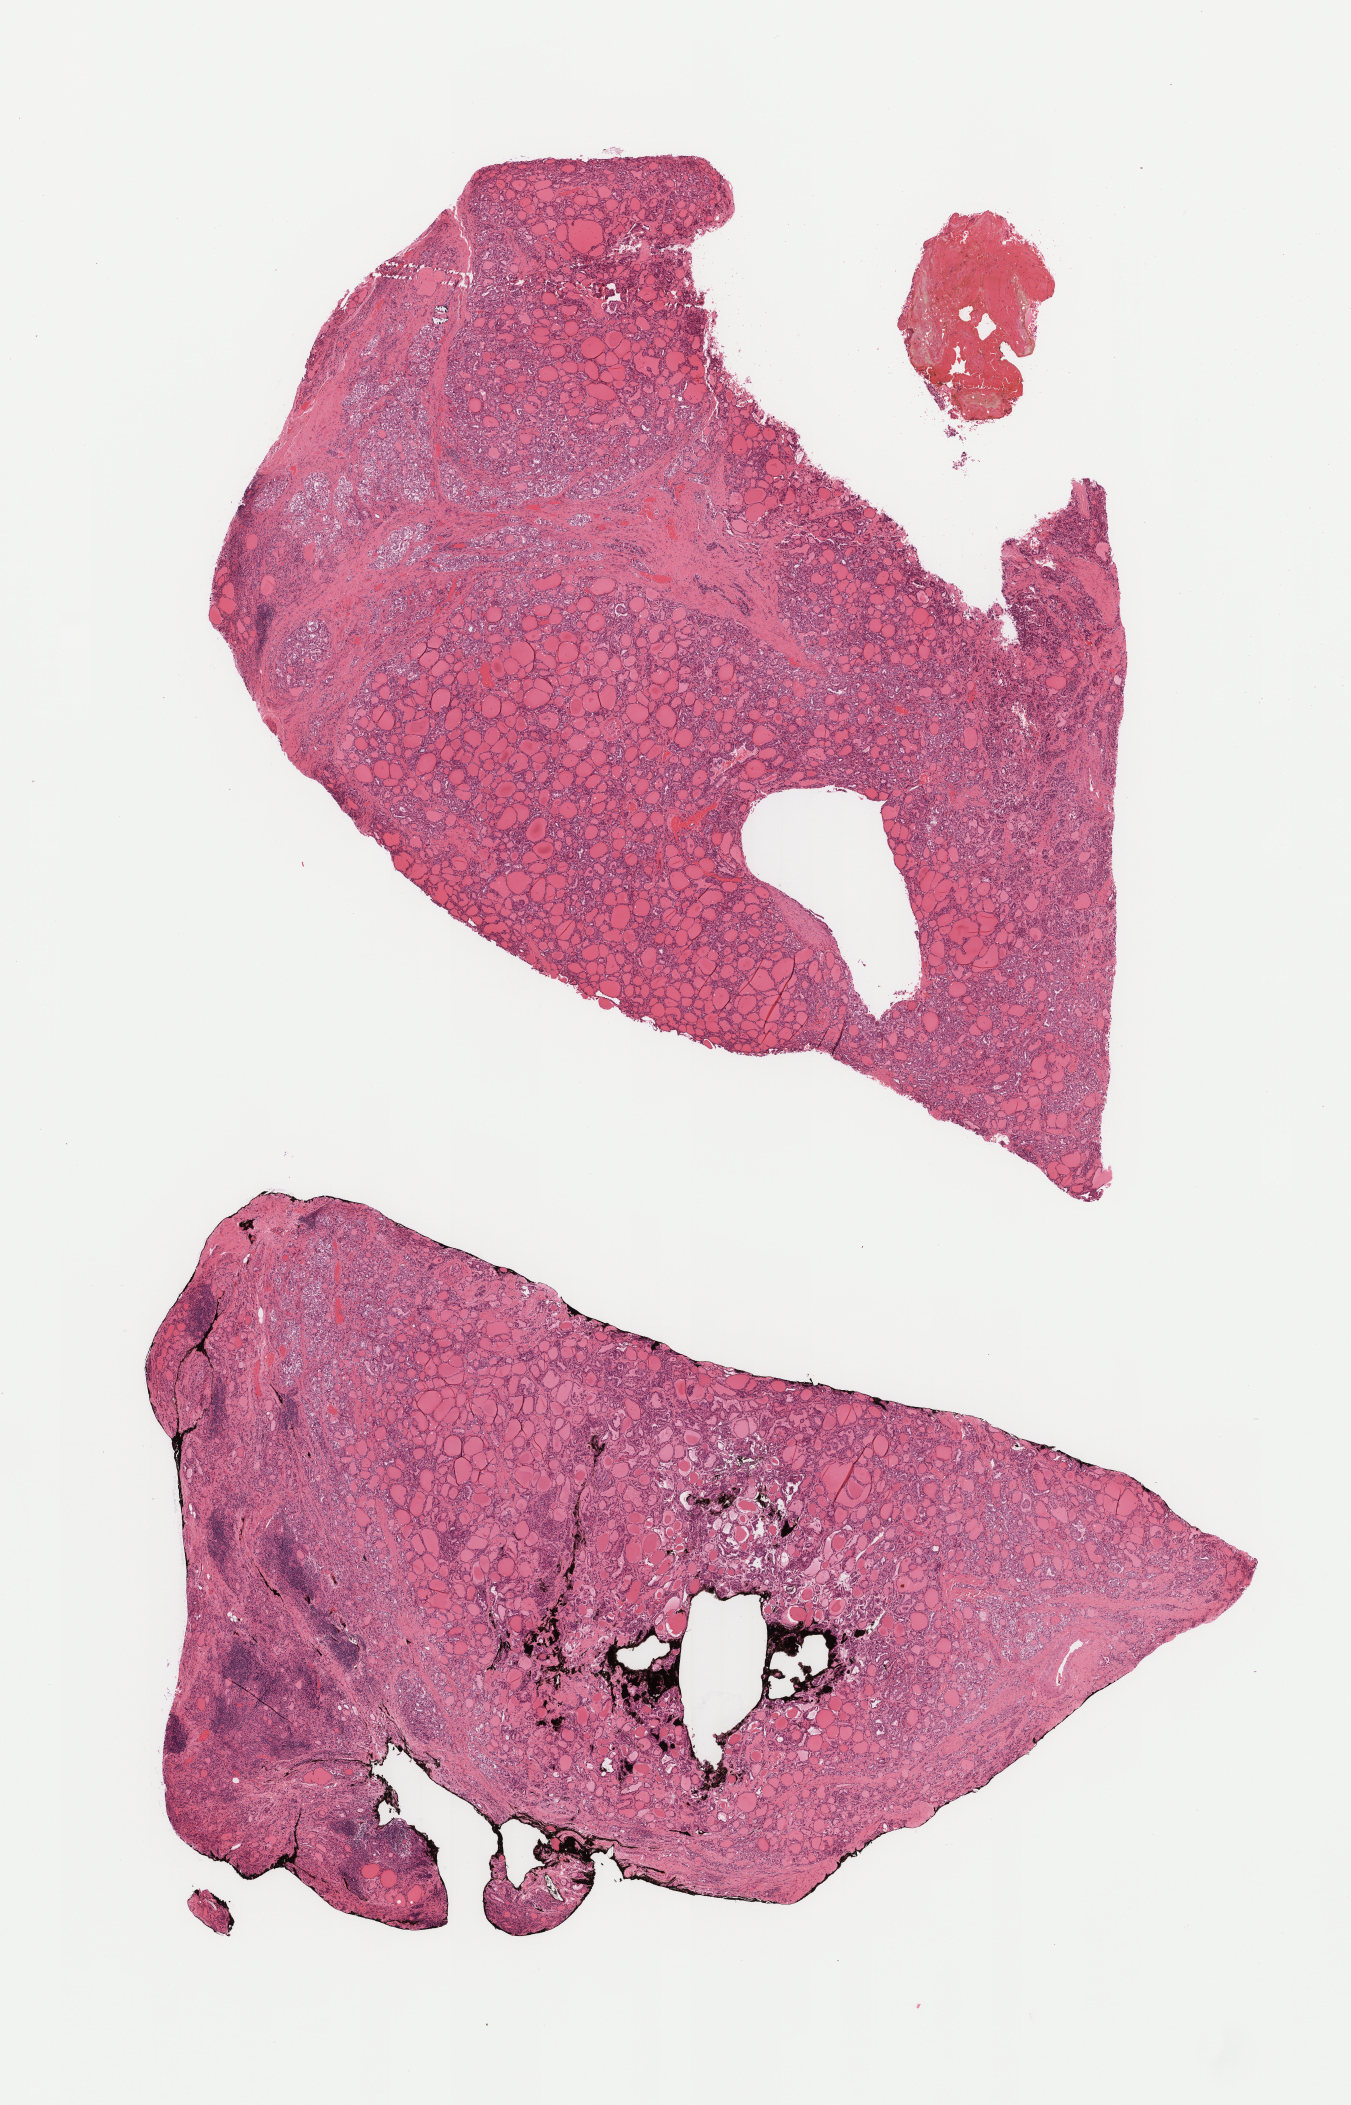
Whole-slide histology image, Hematoxylin and eosin (H&E) stained — whole scanned area (about 10.9 x 17.0 mm, acquisition: 40x scan) shown as a low-resolution overview. Formalin-fixed paraffin-embedded (FFPE) diagnostic section. Sample: primary tumour, thyroid. Patient: female, age at initial diagnosis 47 years.
AJCC pathologic stage: III (7th edition). Diagnosis: Papillary carcinoma, follicular variant (thyroid gland). Lymph nodes positive (case pathology): 4 of 30 examined.